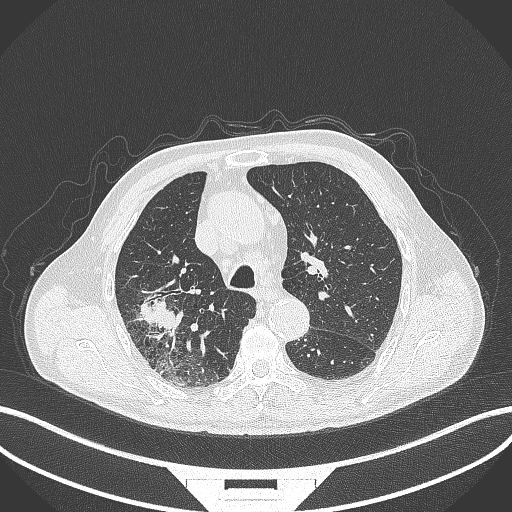
Chest CT, one axial slice. Slice 288 of 429 in the series (ordered by position). Reconstruction kernel B70f. 120 kVp. Lung window (W 1500 / L -600 HU). 512 × 512 image matrix, field of view 400 × 400 mm. Male patient, age 72 years. Case-level facts recorded for this patient, not image findings: clinical TNM (as recorded): T3 N2 M0.
Structures marked on this image (rectangle marked by the reading radiologist):
- lung tumour (recorded histology: adenocarcinoma): bounding box (x1, y1, x2, y2) in pixels: (137, 290, 183, 336)